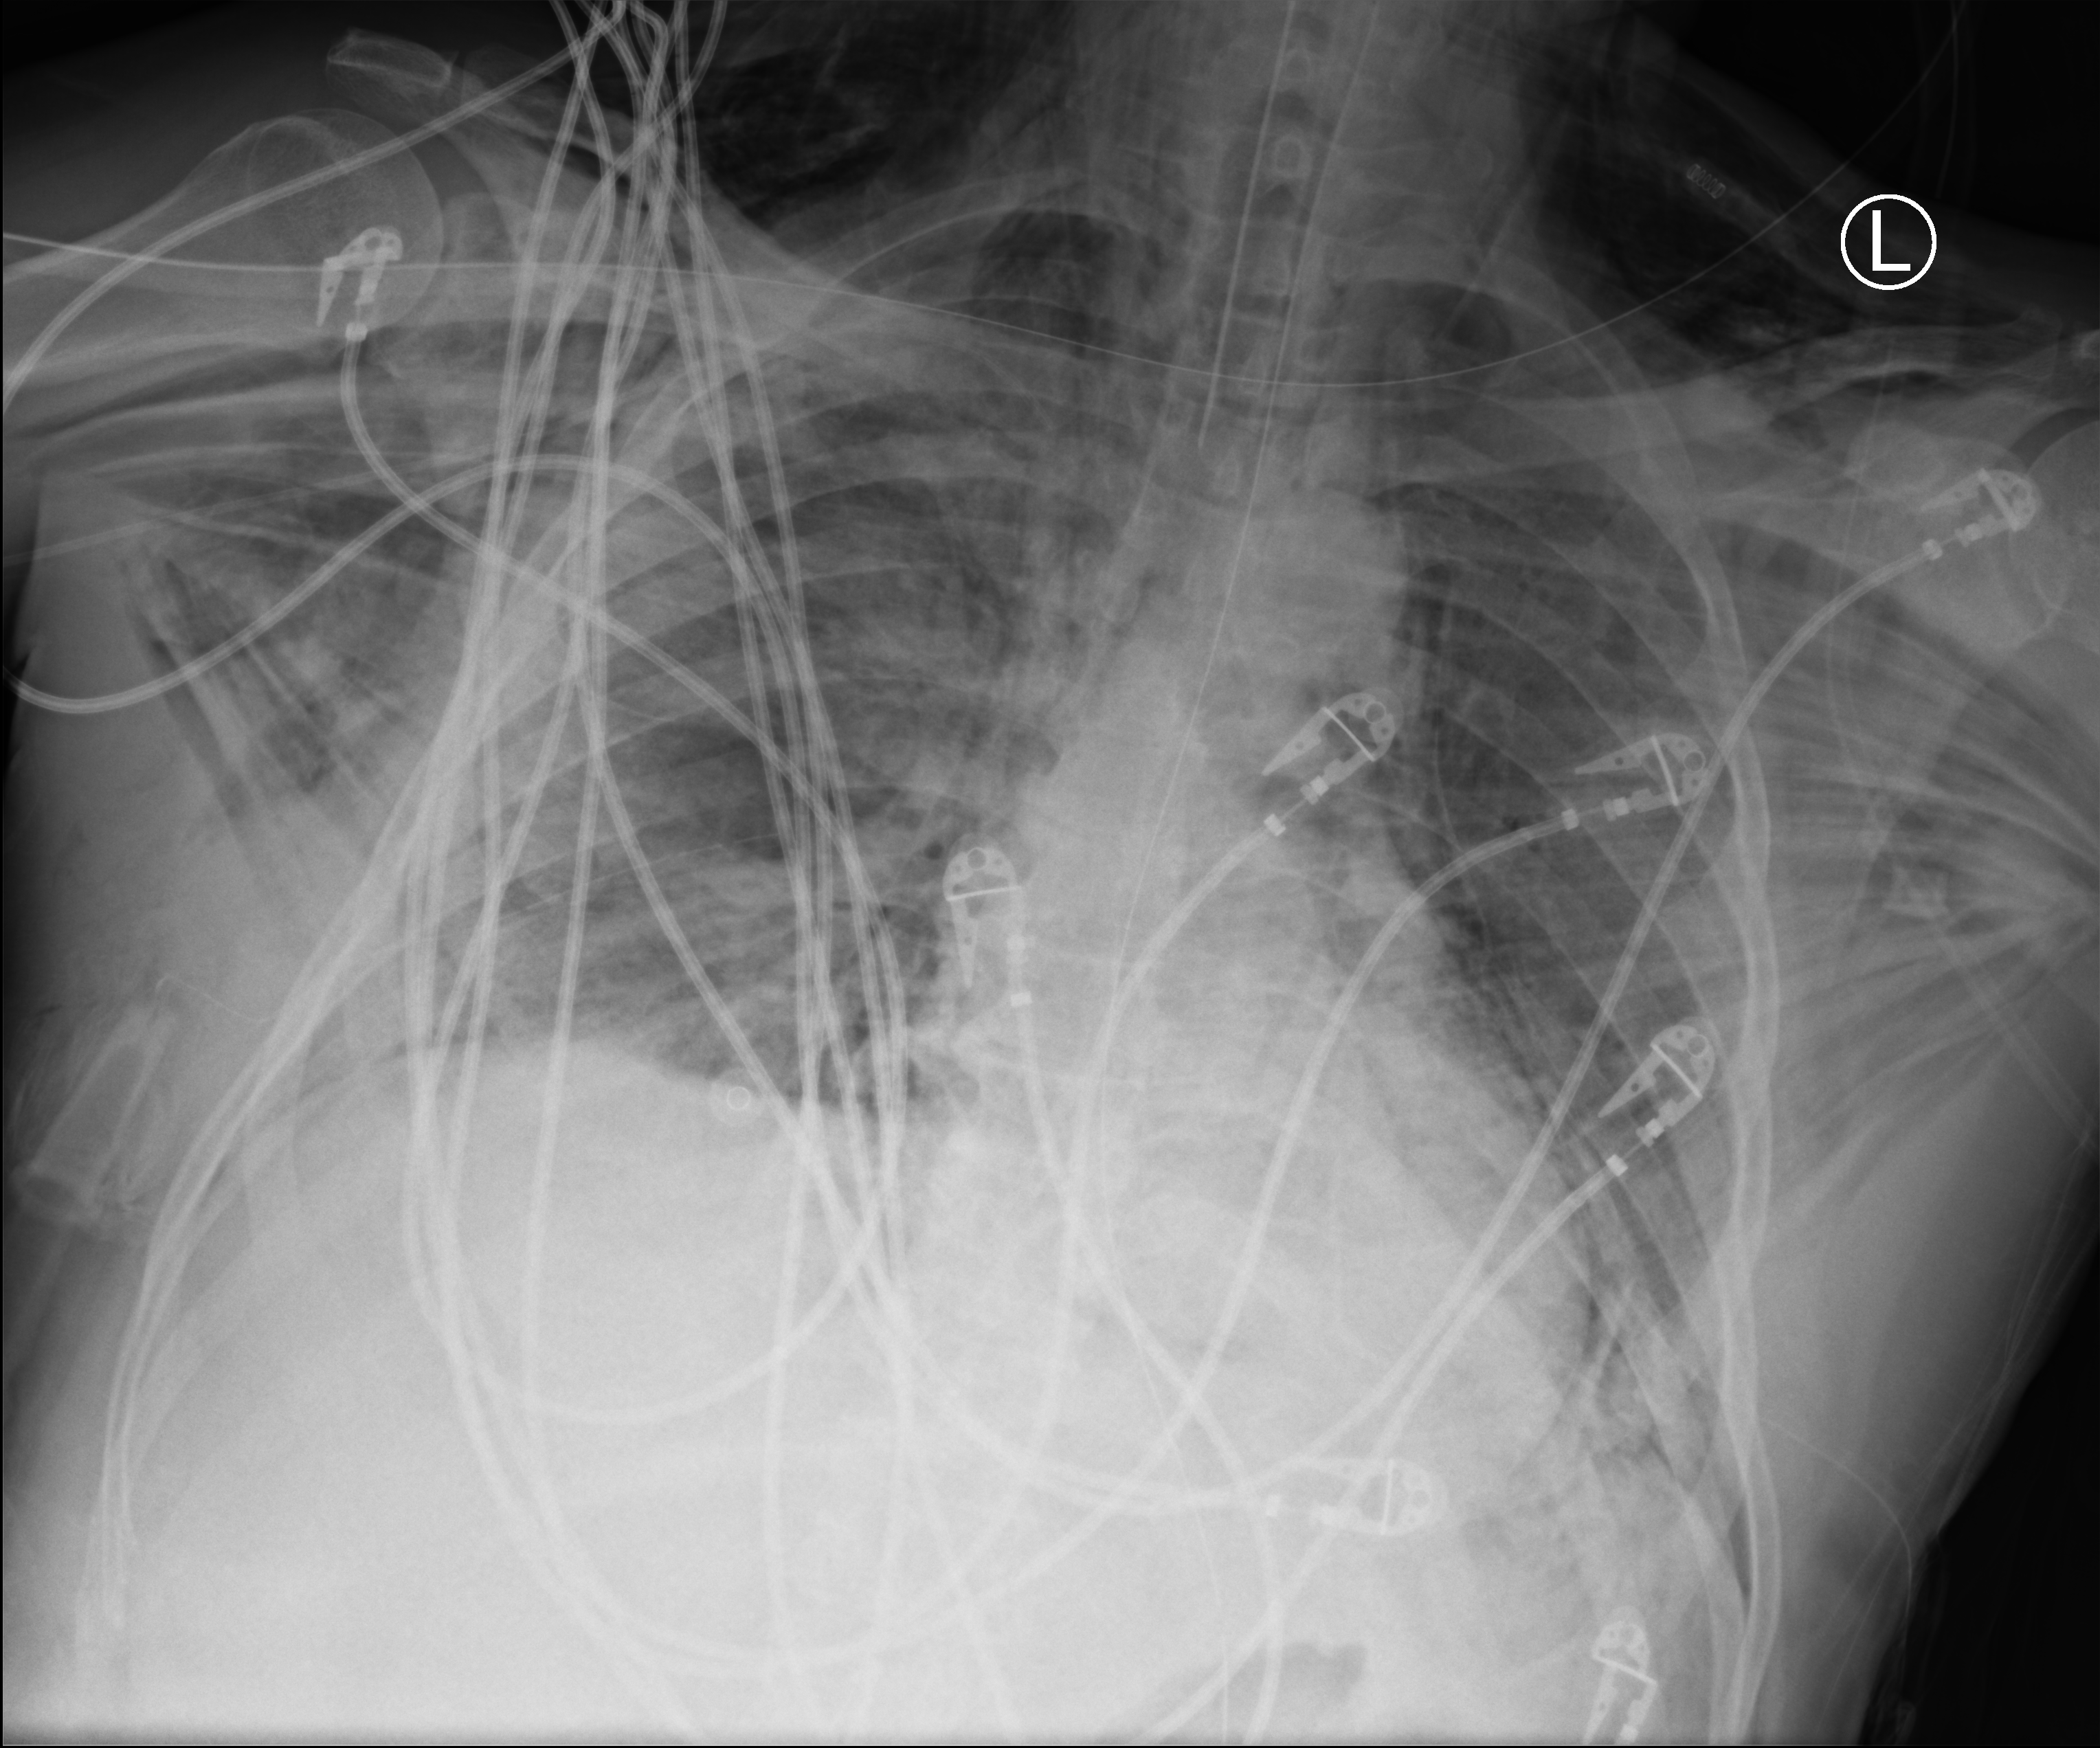
Portable chest radiograph, anteroposterior (AP) projection. Patient hospitalised with COVID-19; male, aged 18–59 years.
Hospital-stay facts (about this admission, not read from this image; timing relative to this image not recorded): length of hospital stay: 83 days.